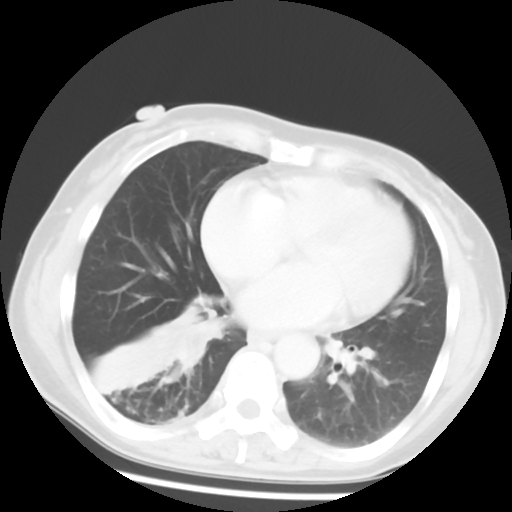
Chest CT, one axial slice; slice 23 of 52 in the series (ordered by position); reconstruction kernel STANDARD; 120 kVp; lung window (W 1500 / L -600 HU); 5 mm slice thickness; 512 × 512 image matrix, field of view 297 × 297 mm. Female patient, age 54 years. From the clinical record (not read from this slice): clinical TNM (as recorded): T1c N0 M0; histopathological grade: G1-2.
Annotated regions visible in this slice (bounding box drawn by a radiologist):
- lung tumour (recorded histology: squamous cell carcinoma): bounding box (x1, y1, x2, y2) in pixels: (168, 296, 228, 383)